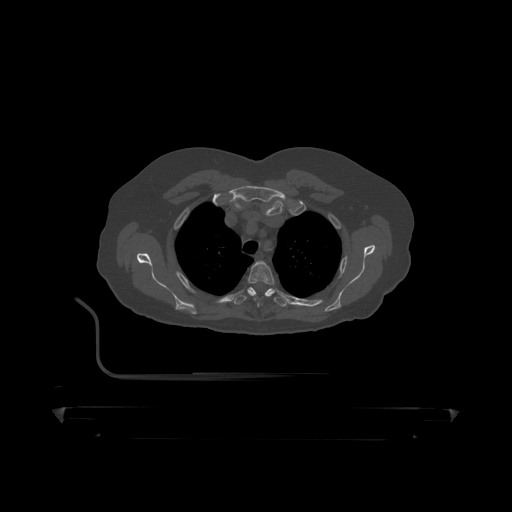
CT including the spine, one axial slice. Slice 351 of 390 in the series (ordered by position). Reconstruction kernel STANDARD. 120 kVp. Bone window (W 1800 / L 400 HU). 1.25 mm slice thickness. 512 × 512 image matrix, field of view 650 × 650 mm. Male patient, age 60 years. From the clinical record (not read from this slice): primary cancer: prostate.
Structures marked on this image (semi-automatic segmentation, software-assisted and operator-edited):
- T3 vertebra: bounding box (x1, y1, x2, y2) in pixels: (248, 262, 276, 286)
- T4 vertebra: (234, 287, 288, 307)